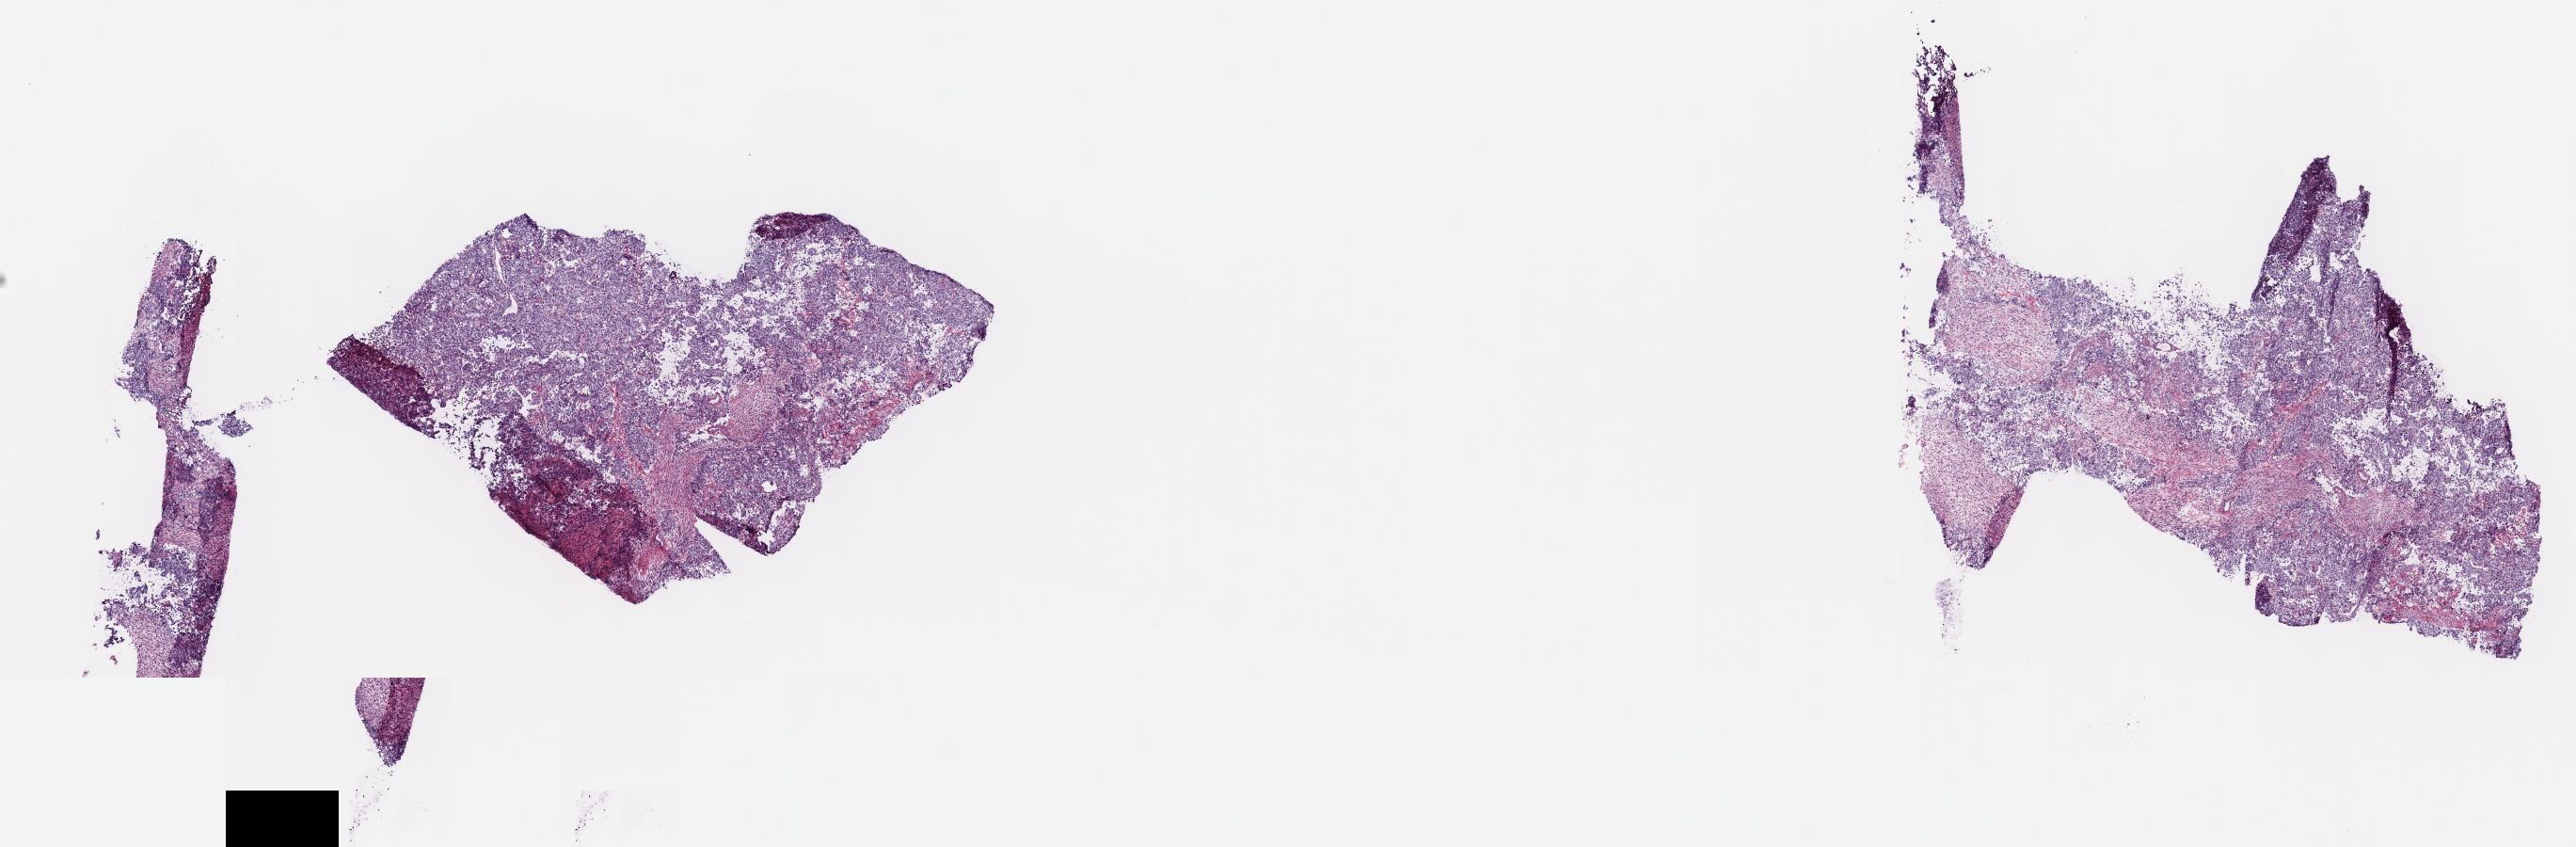
Whole-slide histology image, H&E — low-resolution overview of the scanned area, about 22.1 x 7.3 mm. Frozen section from the top of the tissue portion. Sample: primary tumour, testis. Male patient; age at initial diagnosis 23 years. Slide review estimates, as recorded: tumour cells 100%, tumour nuclei 80%, normal cells 0%, stromal cells 0%, necrosis 0%. Inflammatory infiltration, as recorded: lymphocyte infiltration 2%, monocyte infiltration 0%, neutrophil infiltration 0%.
* histologic diagnosis: Embryonal carcinoma, NOS